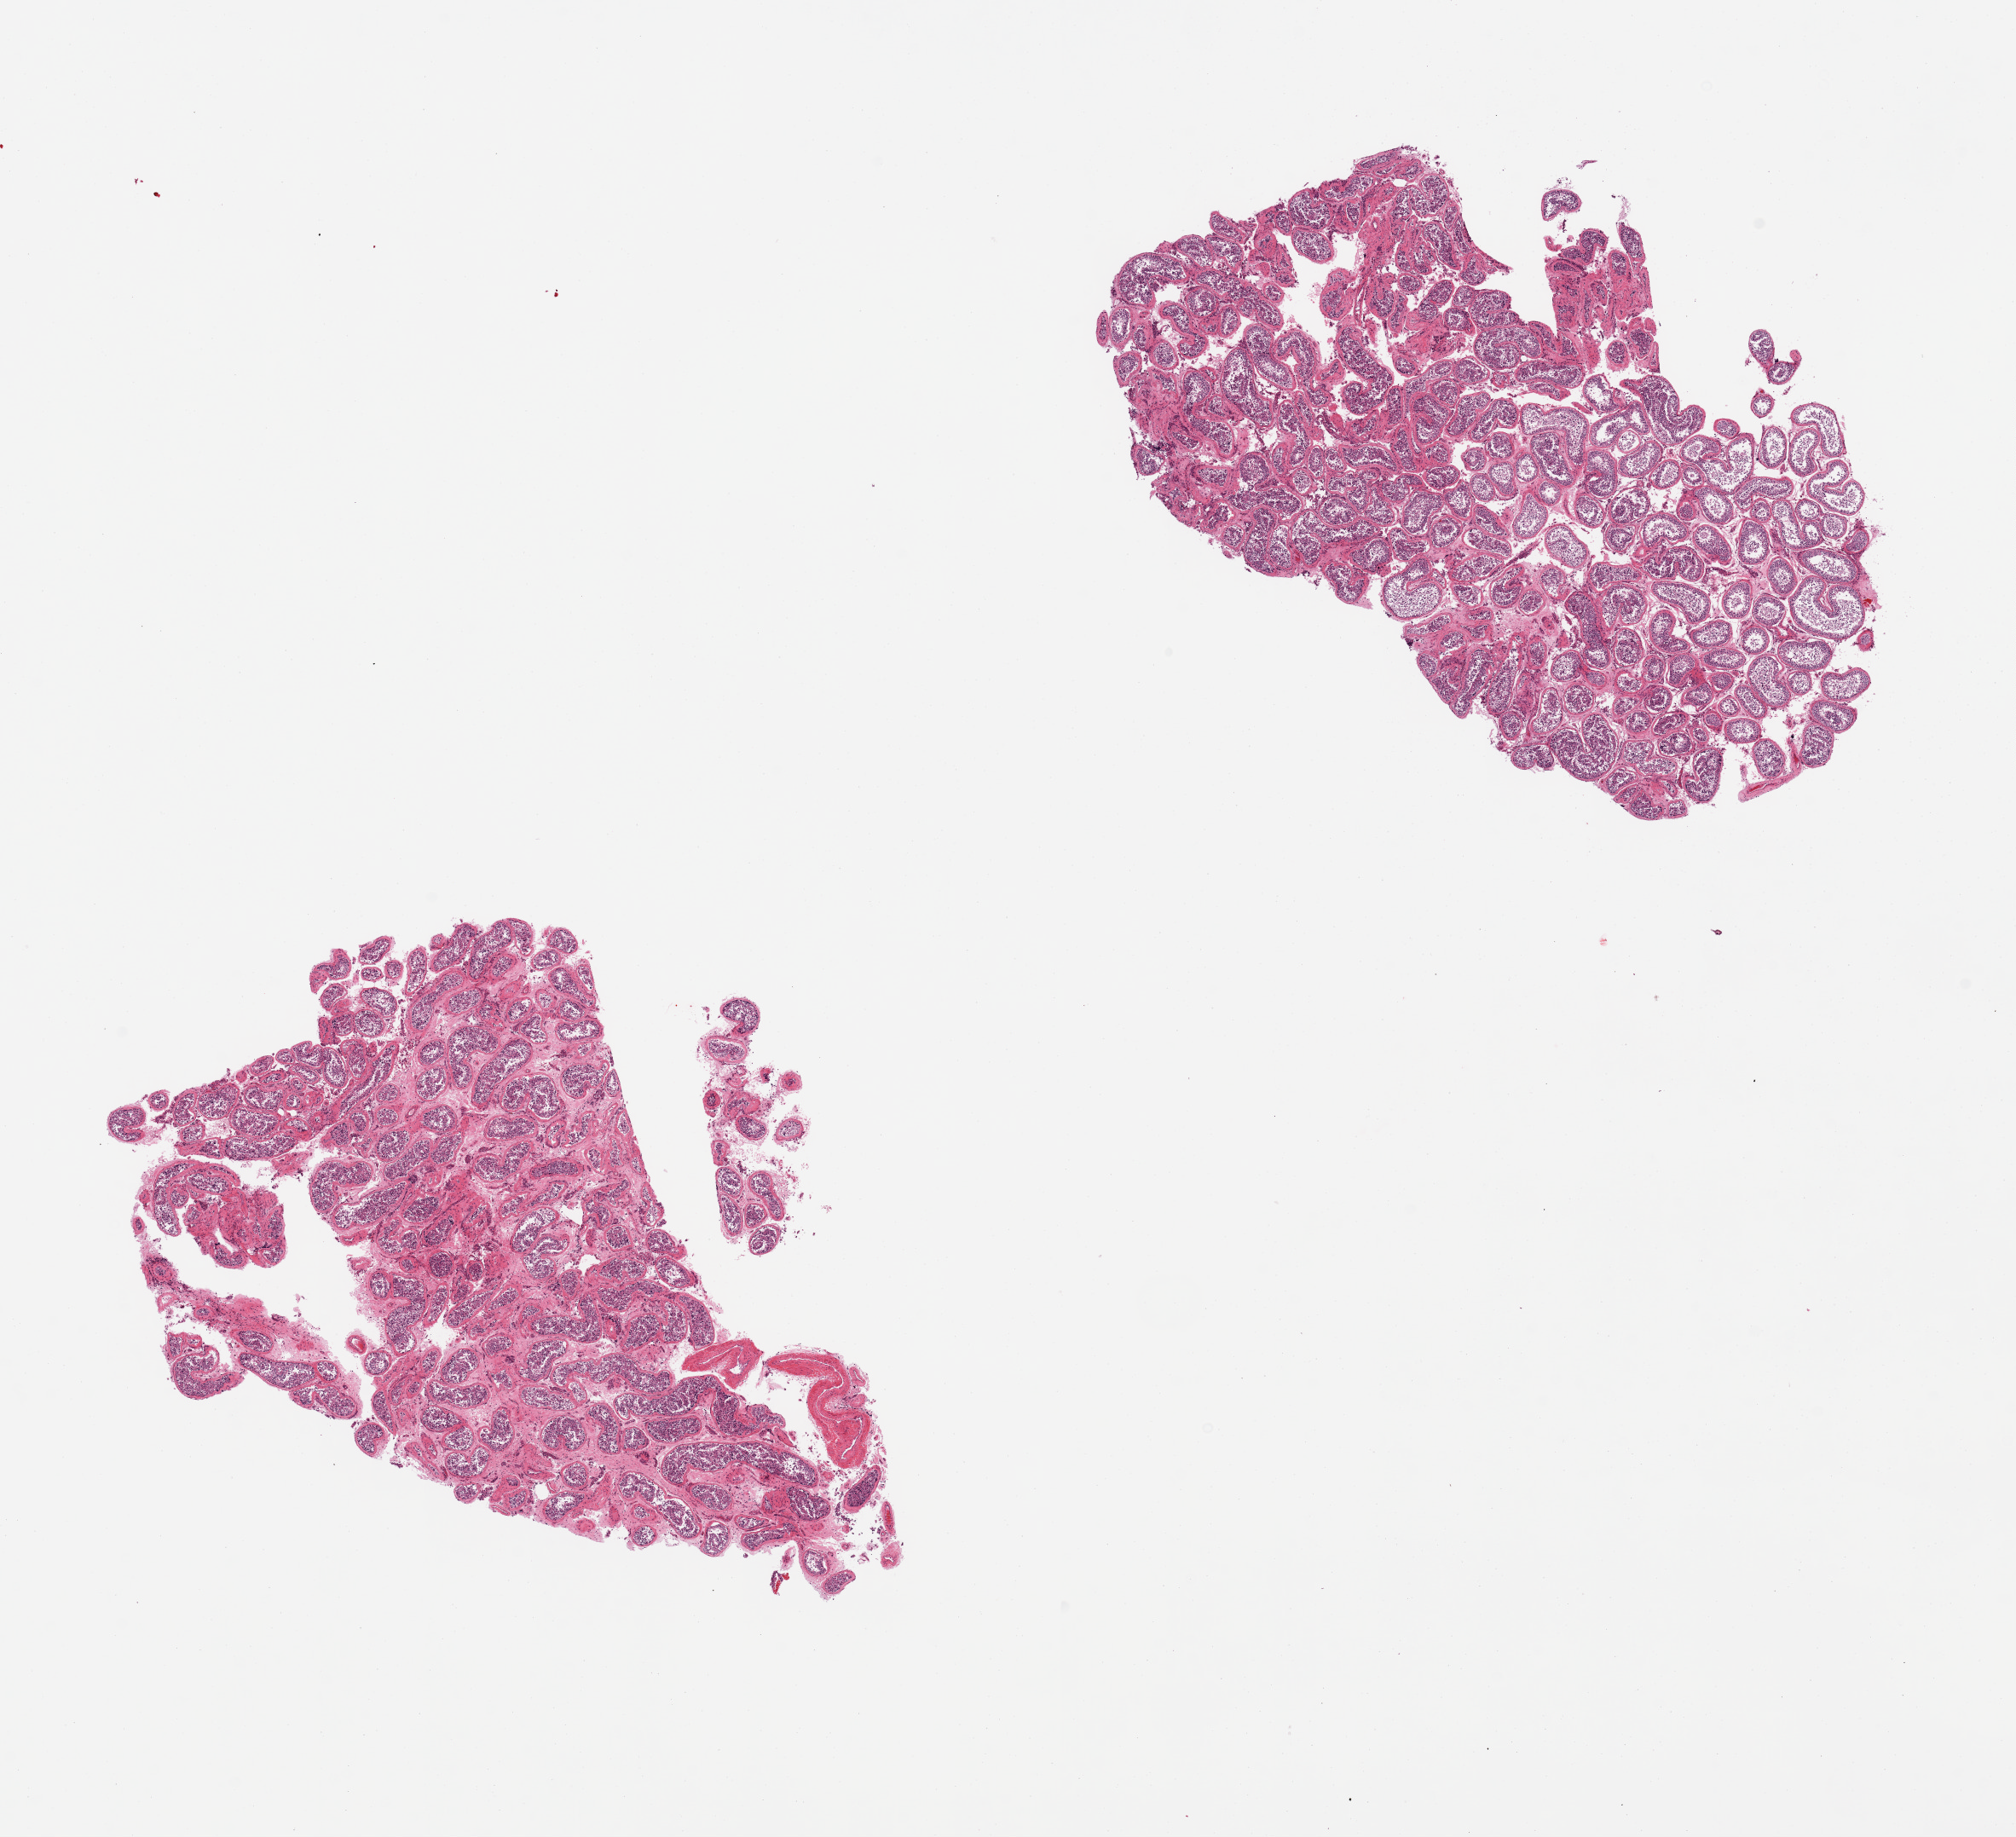
Hematoxylin and eosin (H&E) whole-slide image — shown as a low-resolution overview of the whole scanned area (about 18.7 x 17.0 mm), PAXgene-fixed, paraffin-embedded tissue, section of testis (target tissue), tissue donor sample. Male donor.
Pathologist's review note for this sample: 2 pieces, peritubular fibrosis, spermatogenesis is present.